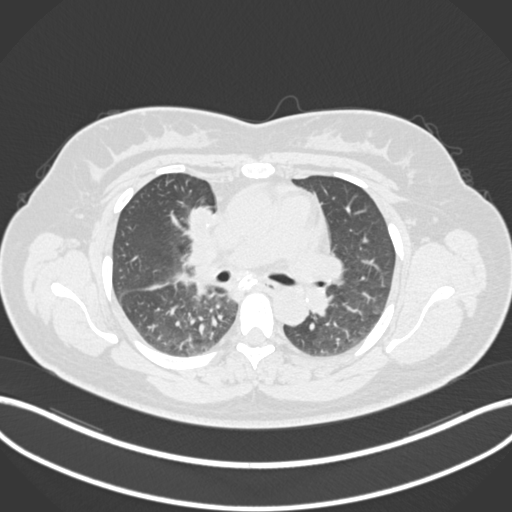
Chest CT, one axial slice; slice 104 of 183 in the series (ordered by position); reconstruction kernel B30f; 120 kVp; lung window (W 1500 / L -600 HU); 1 mm slice thickness; 512 × 512 image matrix. Female patient, age 46 years. From the clinical record (not read from this slice): clinical TNM (as recorded): T2a N1 M0.
Outlined on this slice (bounding box drawn by a radiologist):
- lung tumour (recorded histology: adenocarcinoma): bounding box <182,200,213,235> (left, top, right, bottom; pixels)